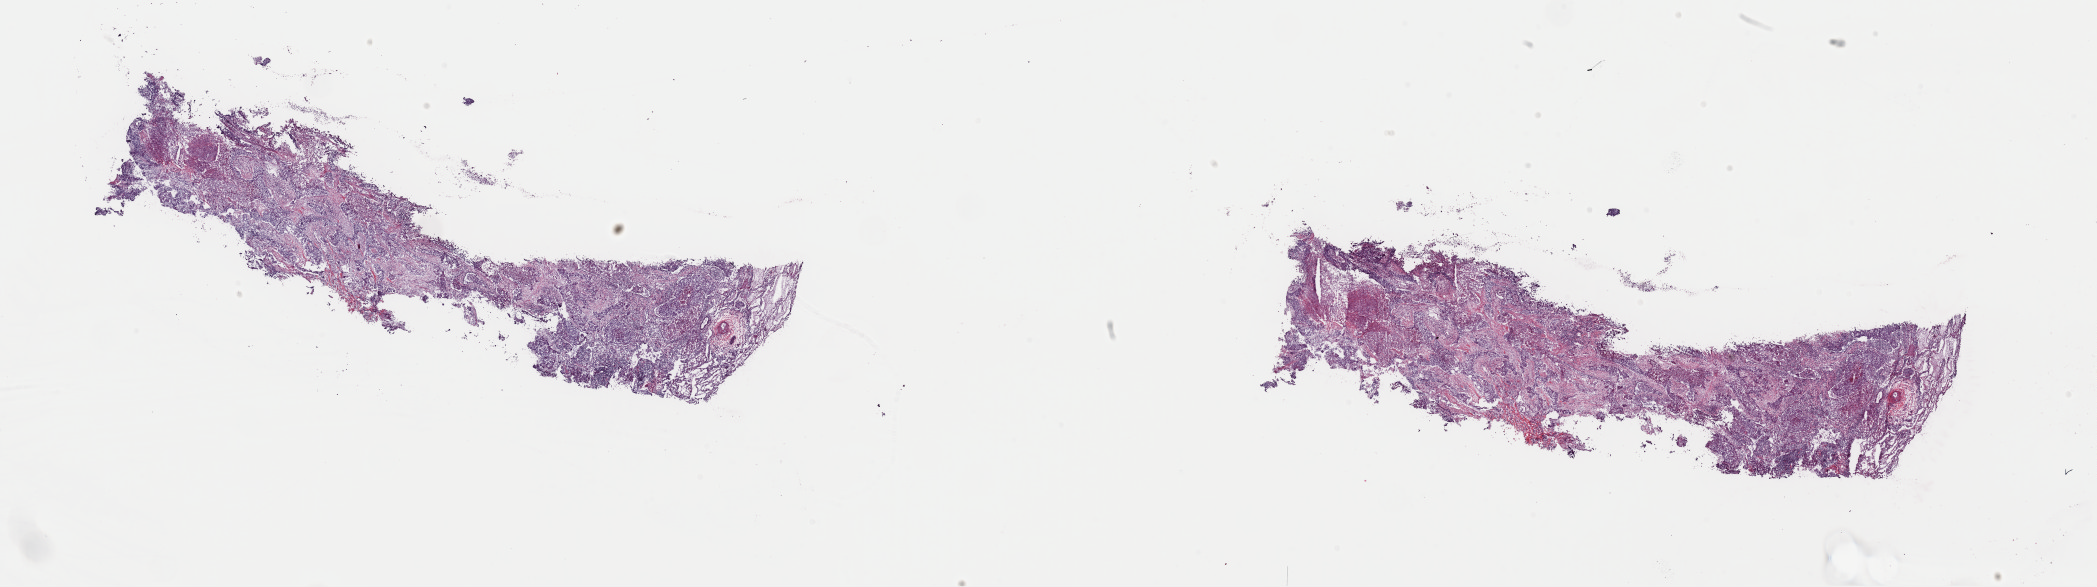
Whole-slide histology image, H&E-stained, a low-resolution overview of the entire scanned area, about 33.1 x 9.3 mm (from a 40x scan). Frozen section from the top of the tissue portion. Primary tumour sample from the lung. Male patient; age at initial diagnosis 63 years. Pathologist review of this section (percent, as recorded): tumour cells 75%, tumour nuclei 65%, normal cells 5%, stromal cells 0%, necrosis 20%. Infiltration values recorded for this section: lymphocyte infiltration 0%, monocyte infiltration 0%, neutrophil infiltration 0%.
- diagnosis: Squamous cell carcinoma, NOS
- AJCC pathologic stage: IIA (7th edition)
- laterality: right